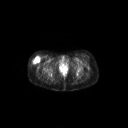
FDG PET of an extremity soft-tissue mass (from a PET/CT study), one axial slice. Position 56 of 267 along the scan axis. 3.27 mm slice thickness. 128 × 128 image matrix, field of view 700 × 700 mm. Female patient, age 34 years. Case-level facts recorded for this patient, not image findings: histological type: synovial sarcoma; grade: intermediate; site of the primary tumour: right thigh.
Annotated regions visible in this slice (expert contour drawn on MRI and transferred to this co-registered scan by the dataset authors):
- gross tumour volume including surrounding oedema: bounding box <31,56,40,64> (left, top, right, bottom; pixels)
- gross tumour volume (mass): <31,56,40,64>